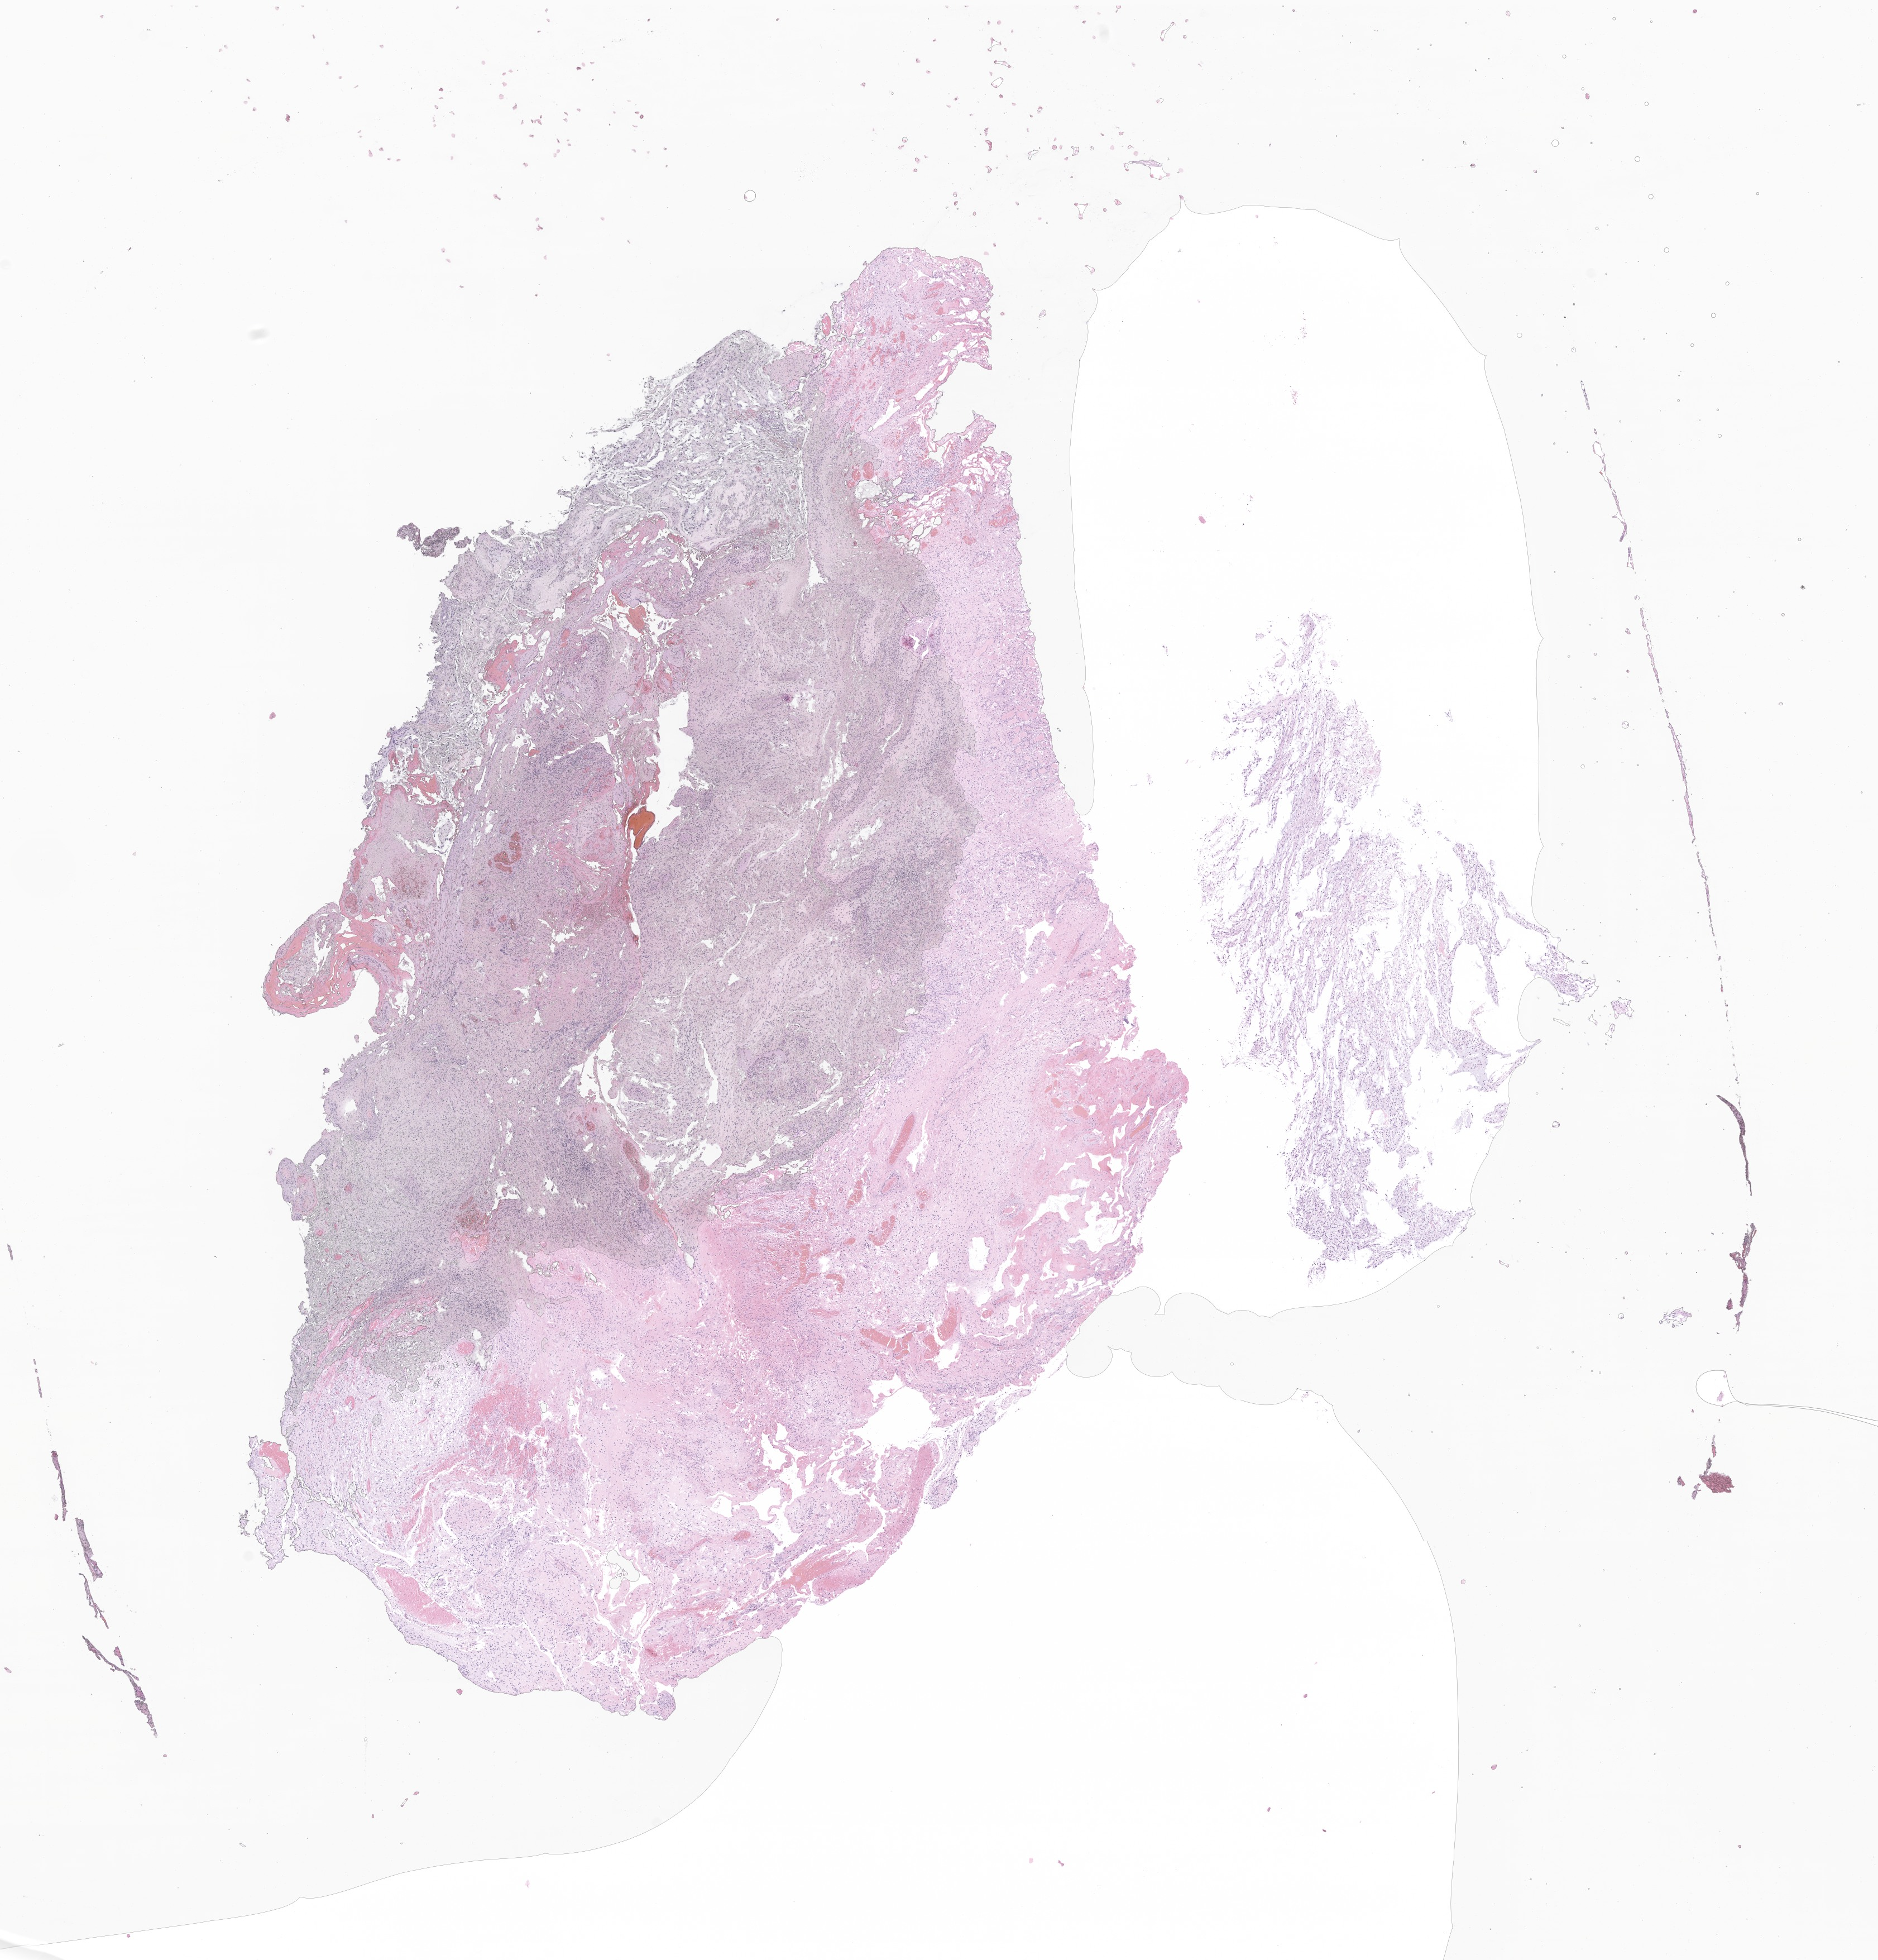
Digitized H&E-stained section of tumor tissue from the temporal lobe, low-resolution overview of the scanned area, about 14.2 x 14.8 mm; FFPE section. Male patient, age 83 months (6 years 11 months).
Recorded diagnosis: Pilocytic astrocytoma.